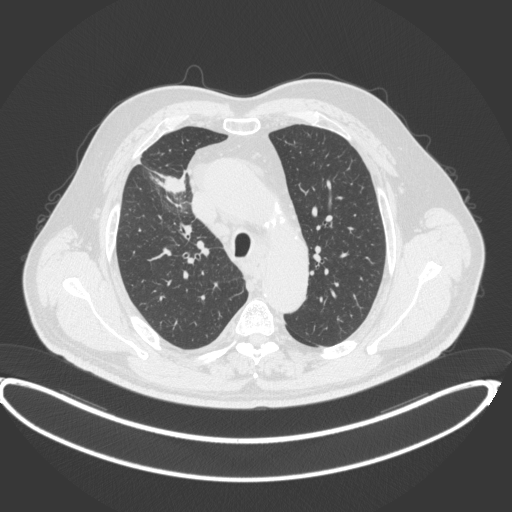
Chest CT, one axial slice. Position 299 of 395 along the scan axis. Reconstruction kernel B31f. Lung window (W 1500 / L -600 HU). 512 × 512 image matrix. Patient: male, 62 years. Case-level facts recorded for this patient, not image findings: clinical TNM (as recorded): T1c N3 M1c.
Outlined on this slice (rectangle marked by the reading radiologist):
- lung tumour (recorded histology: adenocarcinoma): box from (x=160, y=173) to (x=188, y=195) px